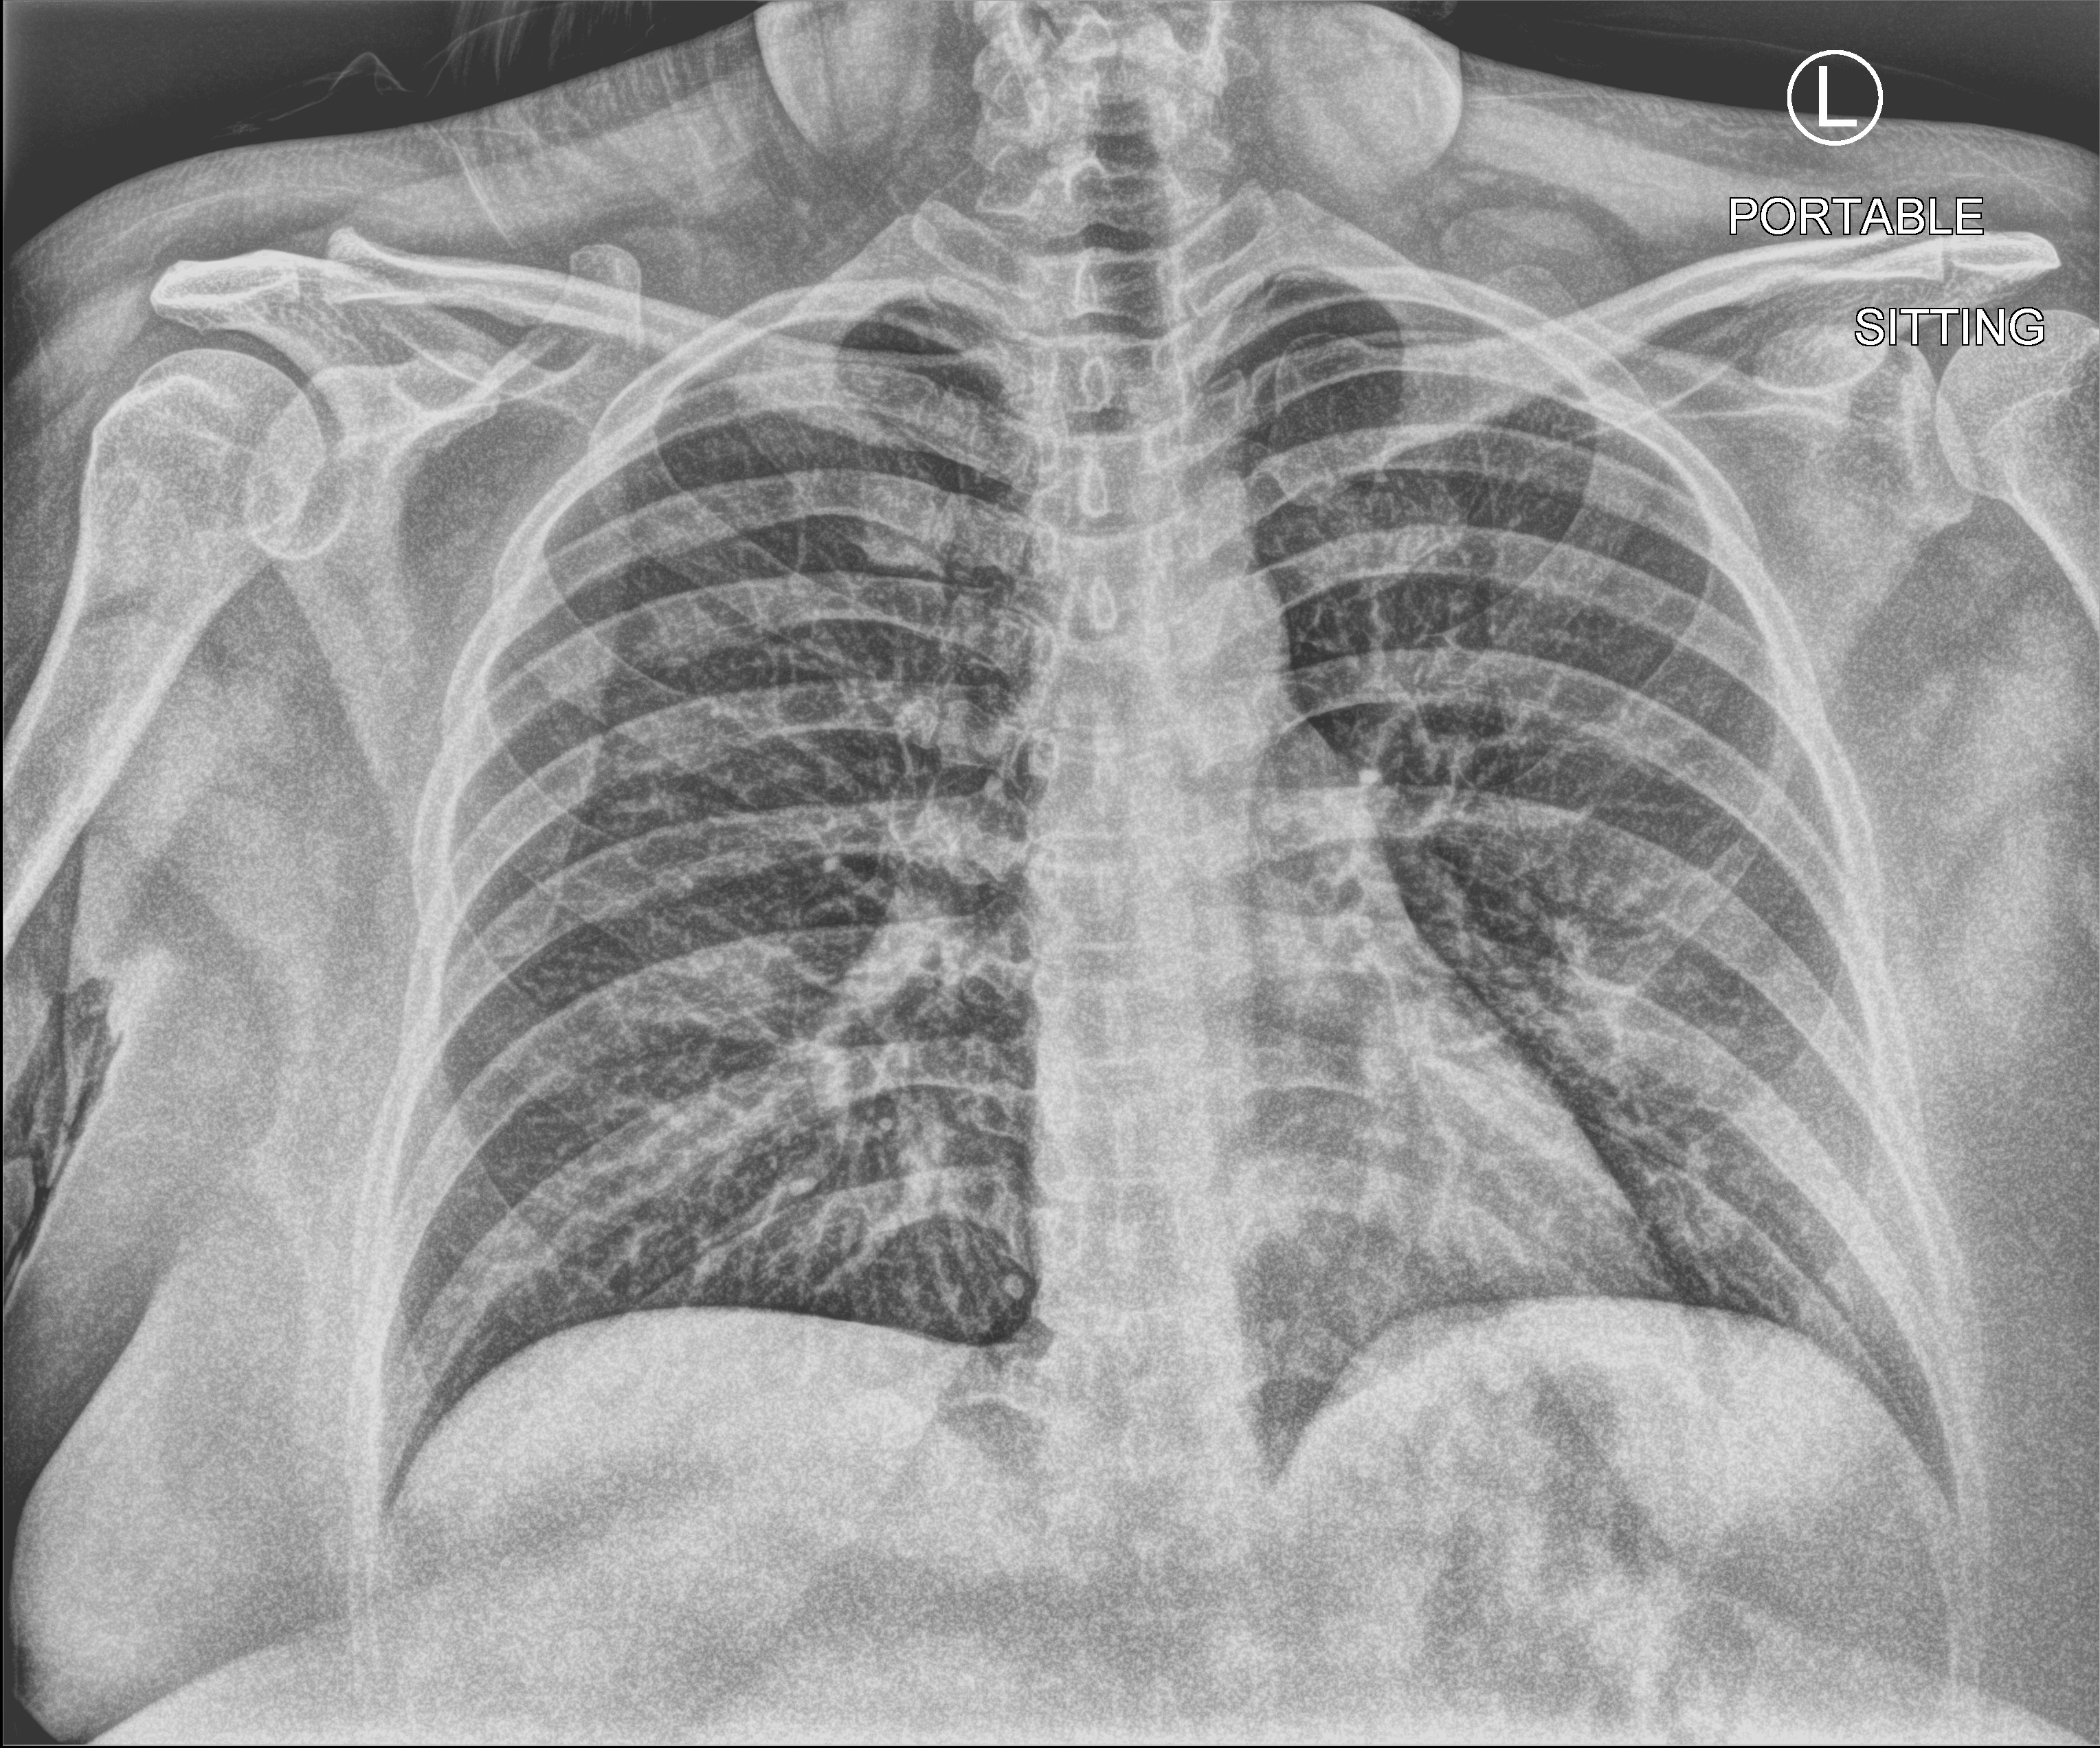
Portable chest radiograph, anteroposterior (AP) projection. Patient hospitalised with COVID-19; female, aged 18–59 years.
From the hospital-stay record, not from the radiograph (when in the stay this image was taken is not recorded):
- admitted to intensive care during this hospital stay: no
- diabetes (admission record): no
- mechanically ventilated during this hospital stay: no